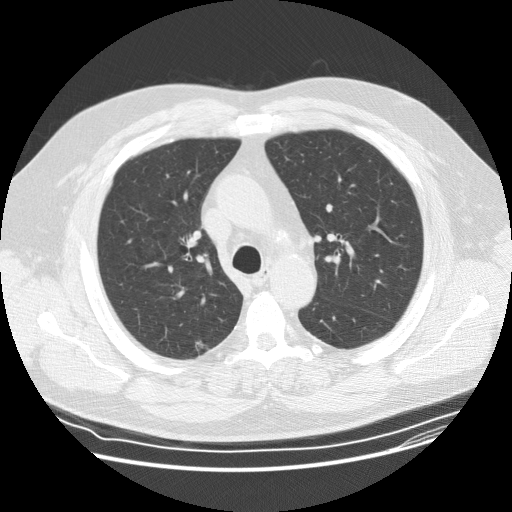
Axial slice from a low-dose chest CT screening exam; baseline screening round; lung window (W 1500 / L -600 HU); 2.5 mm slice thickness; slice 48 of 162 in the series; 512 × 512 image matrix. Male participant, aged 62 years at enrolment. Former smoker at enrolment.
Expert-annotated lung lesion, bounding box [x1, y1, x2, y2] px = [181, 328, 218, 370]. Screening reader's record for this exam (one nodule recorded; not confirmed to be the boxed lesion): non-calcified nodule or mass ≥4 mm, right upper lobe, 8 × 7 mm, smooth margins, ground glass attenuation. Official screen result: positive, change unspecified: nodule(s) >= 4 mm or enlarging nodule(s), mass(es), or other non-specific abnormalities suspicious for lung cancer. Participant outcome: lung cancer diagnosed 795 days after this screen — bronchiolo-alveolar adenocarcinoma, NOS, right upper lobe, well differentiated (G1), stage IA (AJCC 6th edition), 12 mm at pathology.